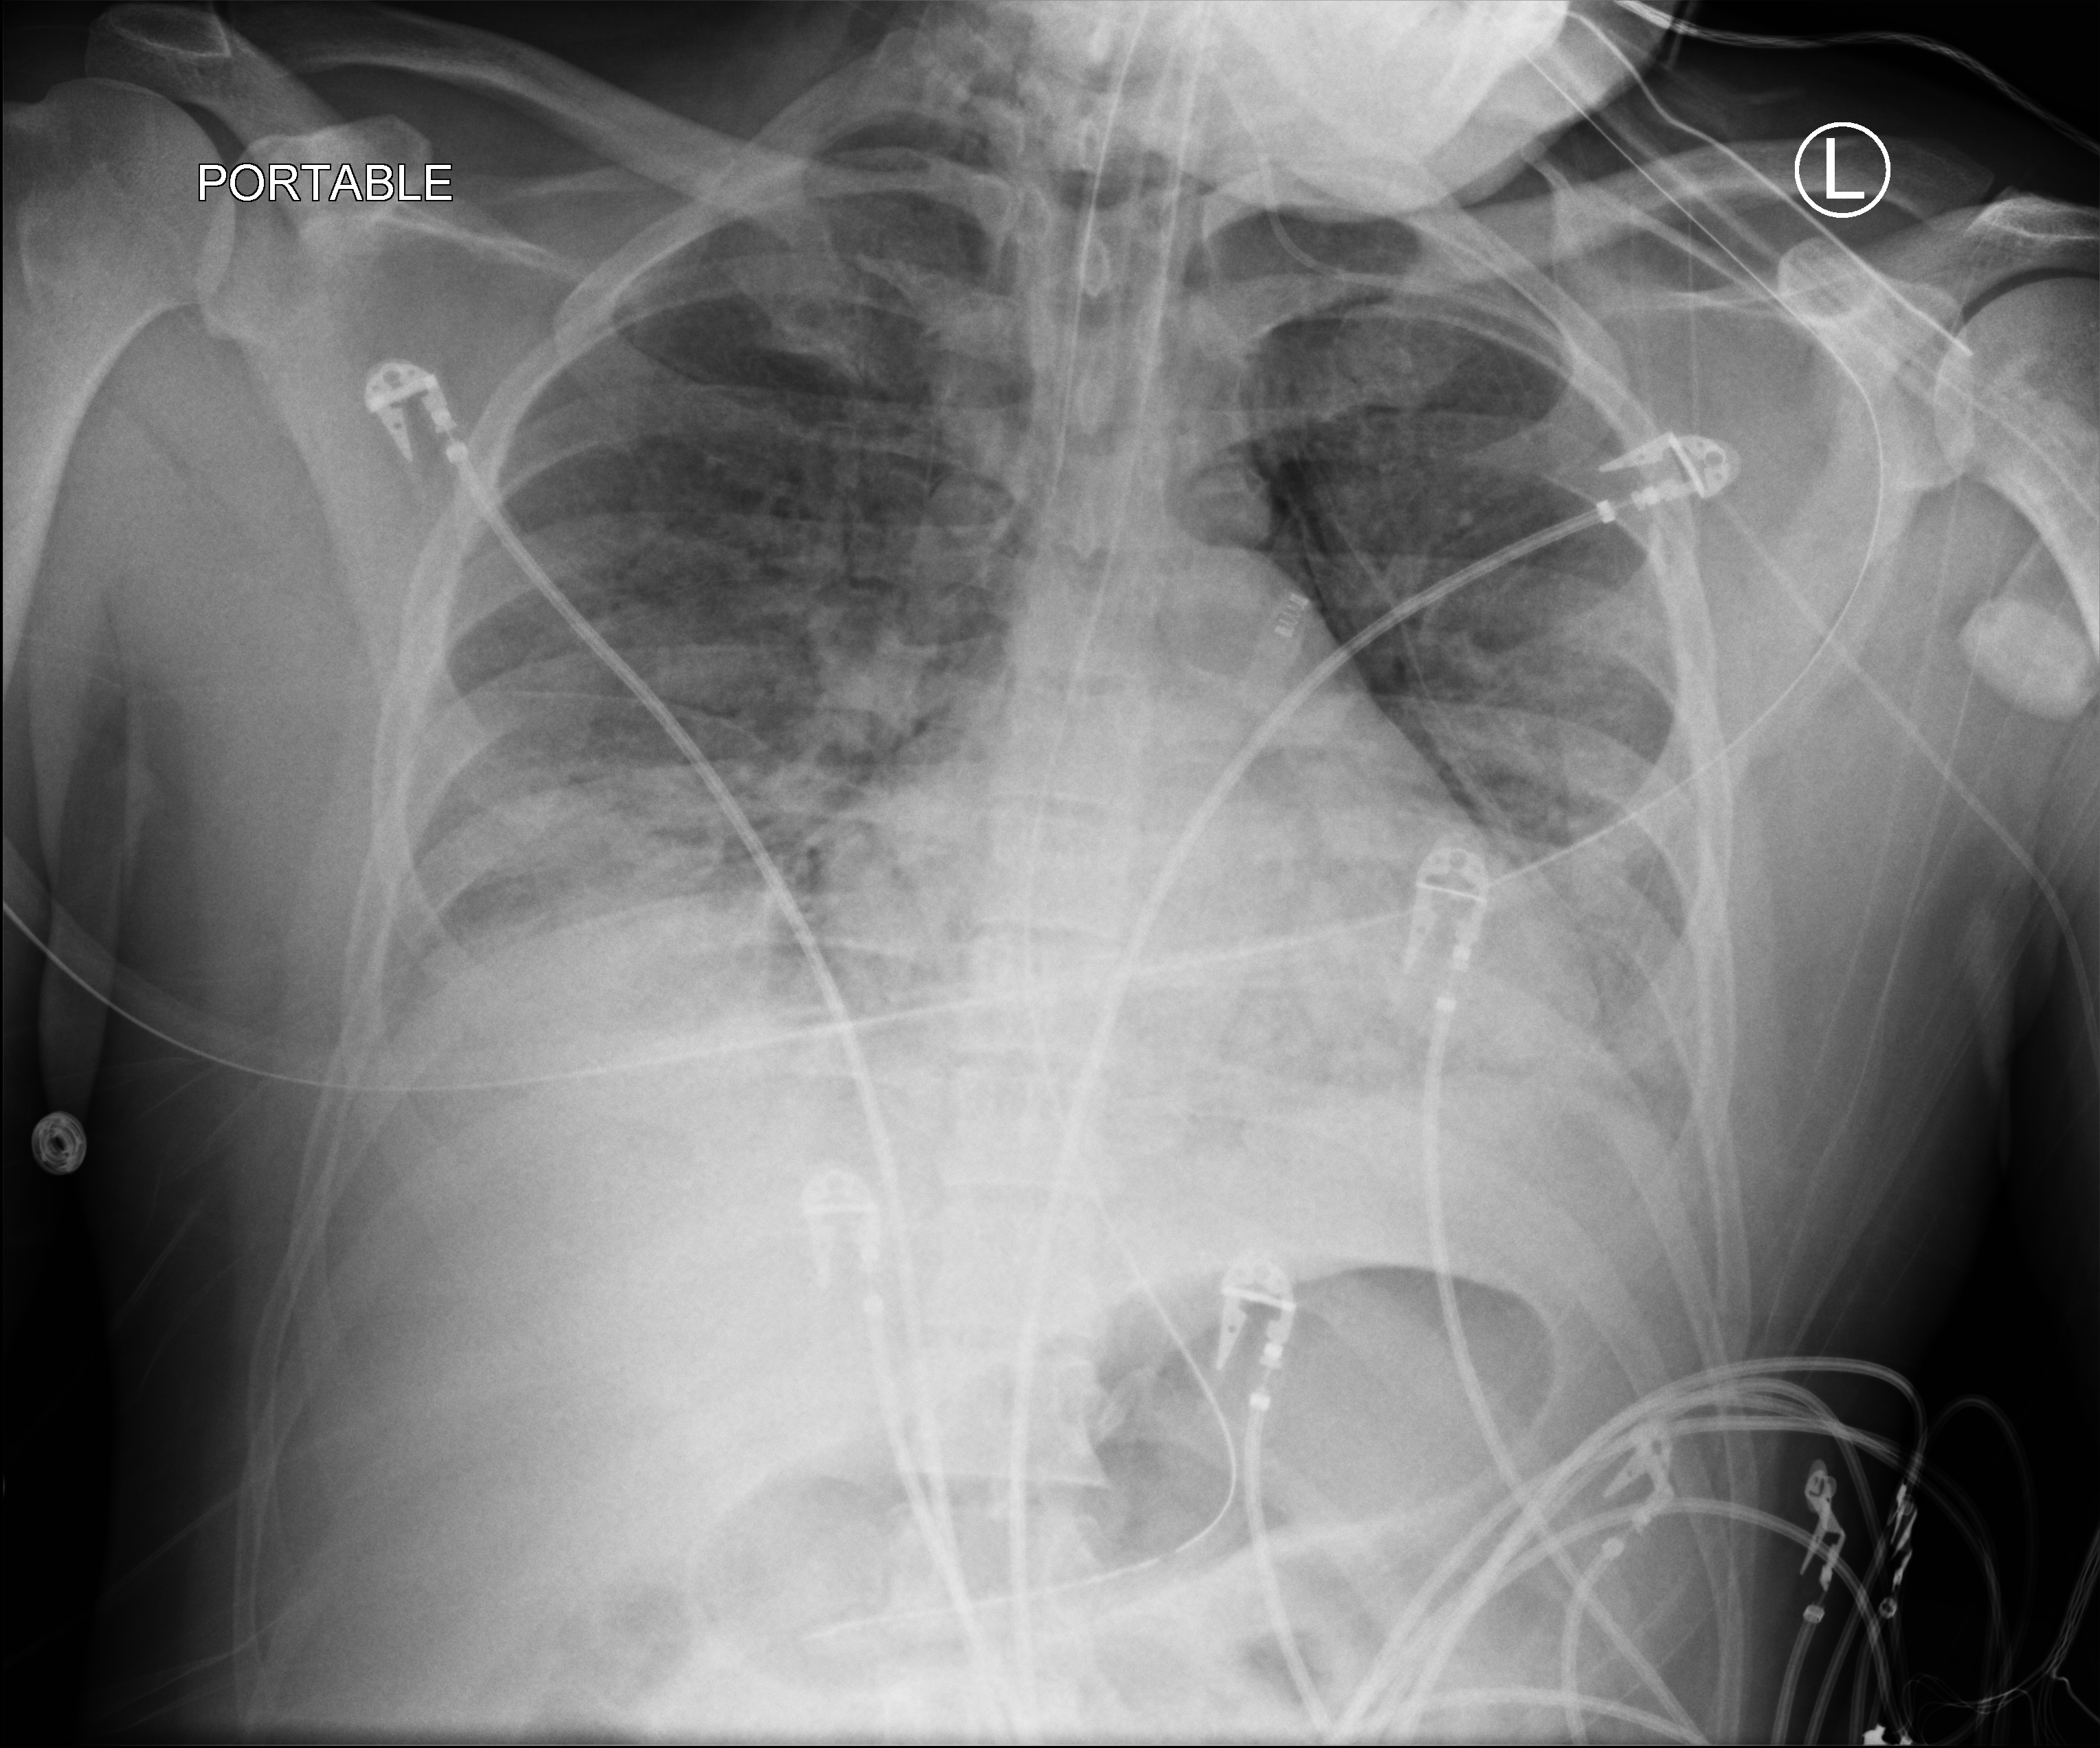
Bedside chest radiograph (computed radiography), anteroposterior (AP) projection. Male patient hospitalised with COVID-19, age 18–59 years.
Admission-level facts for this patient (not findings on this image; timing relative to this image not recorded):
- mechanically ventilated during this hospital stay: yes